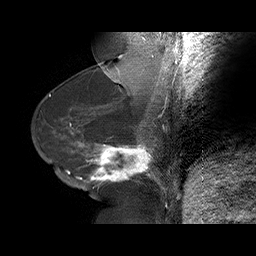
Breast MRI (dynamic contrast-enhanced), one sagittal slice. Position 30 of 75 along the scan axis. Dynamic contrast-enhanced series, time point 2 of 6 at this slice position (early post-contrast). 1.5 T. TE 4.5 ms, TR 32.4 ms. 256 × 256 image matrix. Female patient. Case-level facts recorded for this patient, not image findings: setting: breast cancer imaged before/during neoadjuvant chemotherapy; receptor status: HR-positive, HER2-negative.
Annotated regions visible in this slice (semi-automatic segmentation, software-assisted and operator-edited):
- analysis volume of interest (the breast-tissue region the enhancement analysis was run in; not a lesion): bounding box <58,134,166,191> (left, top, right, bottom; pixels)
- tumour enhancement mask (voxels above the 100 % enhancement threshold inside the analysis volume of interest): <66,141,165,189>